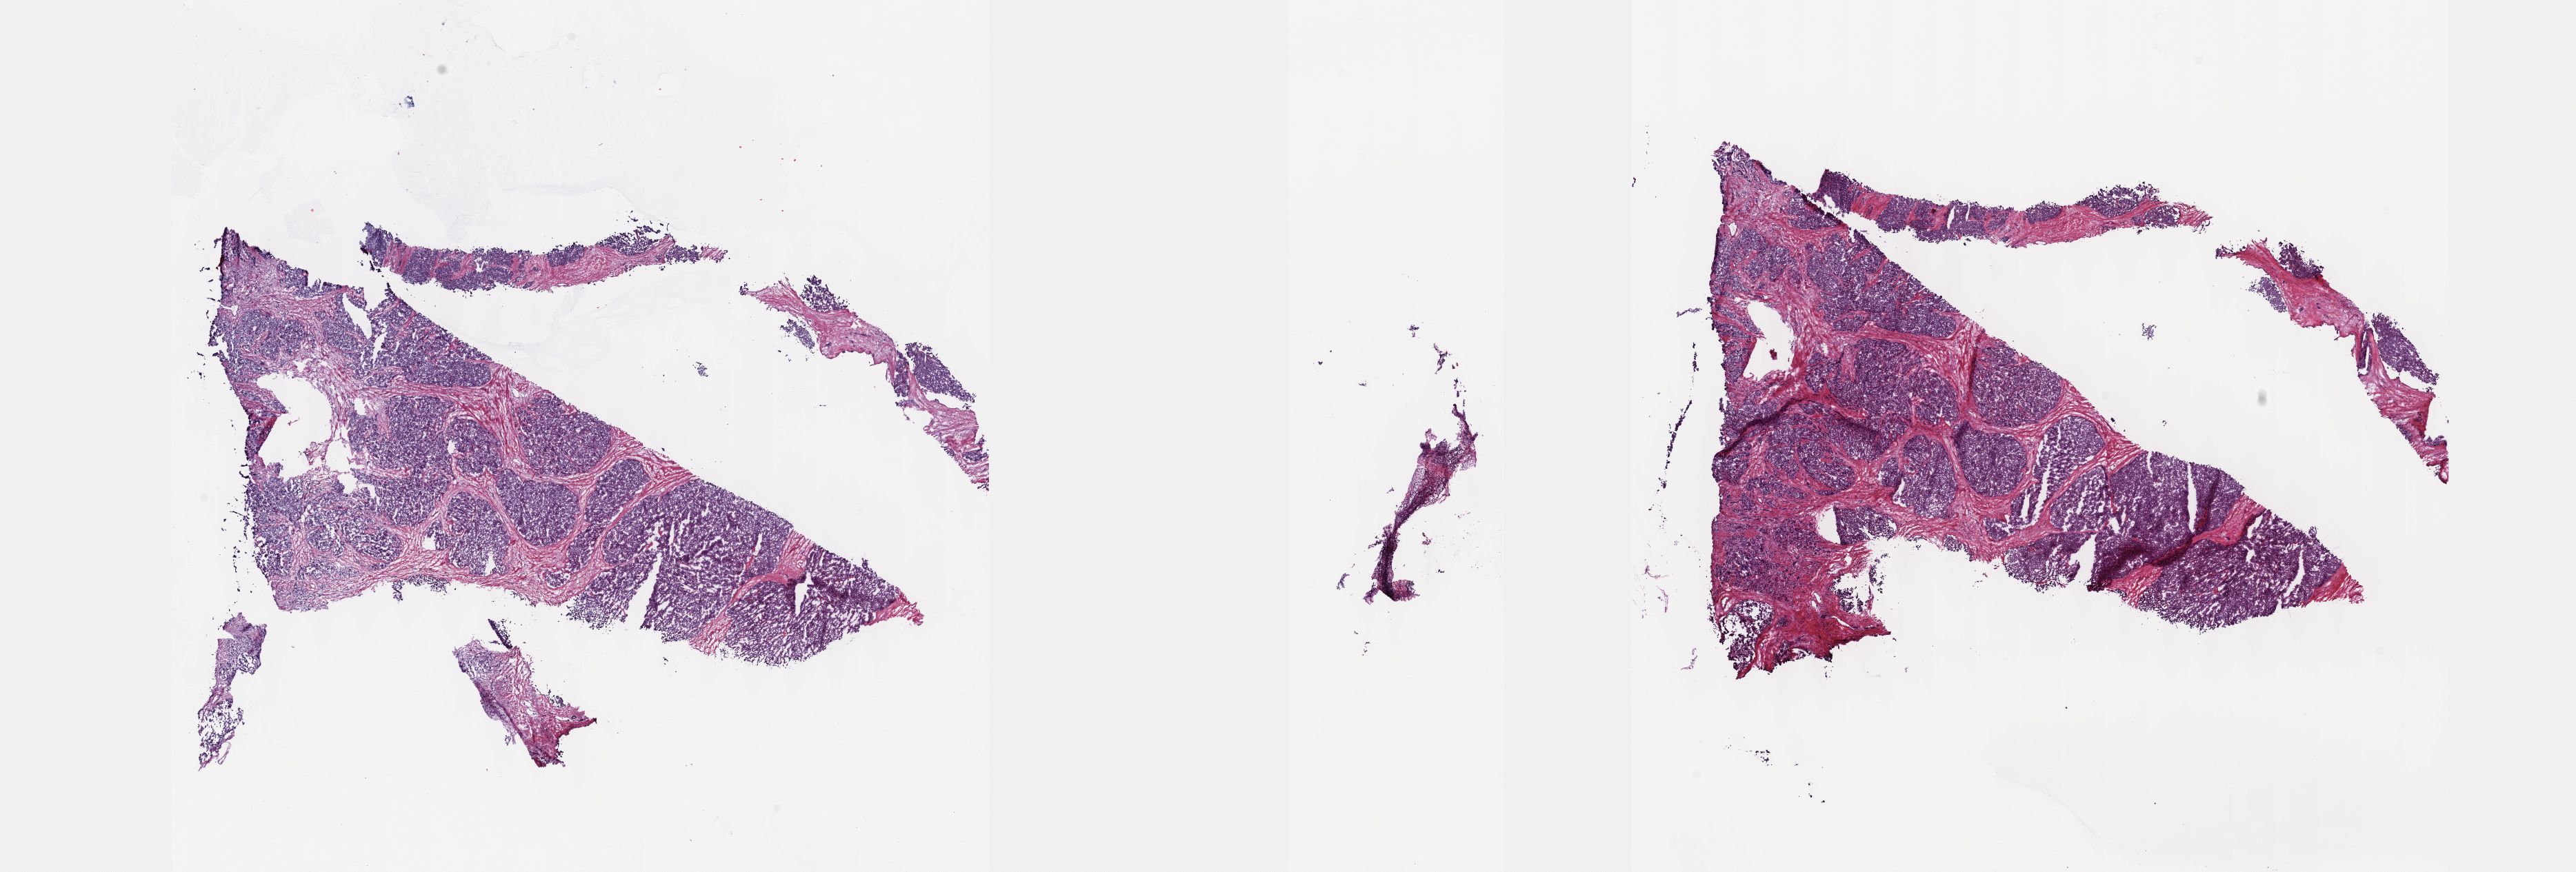
H&E whole-slide image — shown as a low-resolution overview of the whole scanned area (about 30.2 x 10.2 mm, acquisition: 40x scan), frozen section from the top of the tissue portion, sample: primary tumour, prostate. Male patient; age at initial diagnosis 58 years. Gleason score: 9 (4+5). Slide review estimates, as recorded: tumour cells 70%, tumour nuclei 75%, normal cells 0%, stromal cells 30%, necrosis 0%. Inflammatory infiltration, as recorded: lymphocyte infiltration 0%, monocyte infiltration 0%, neutrophil infiltration 0%.
Diagnosis: Adenocarcinoma, NOS (prostate gland).